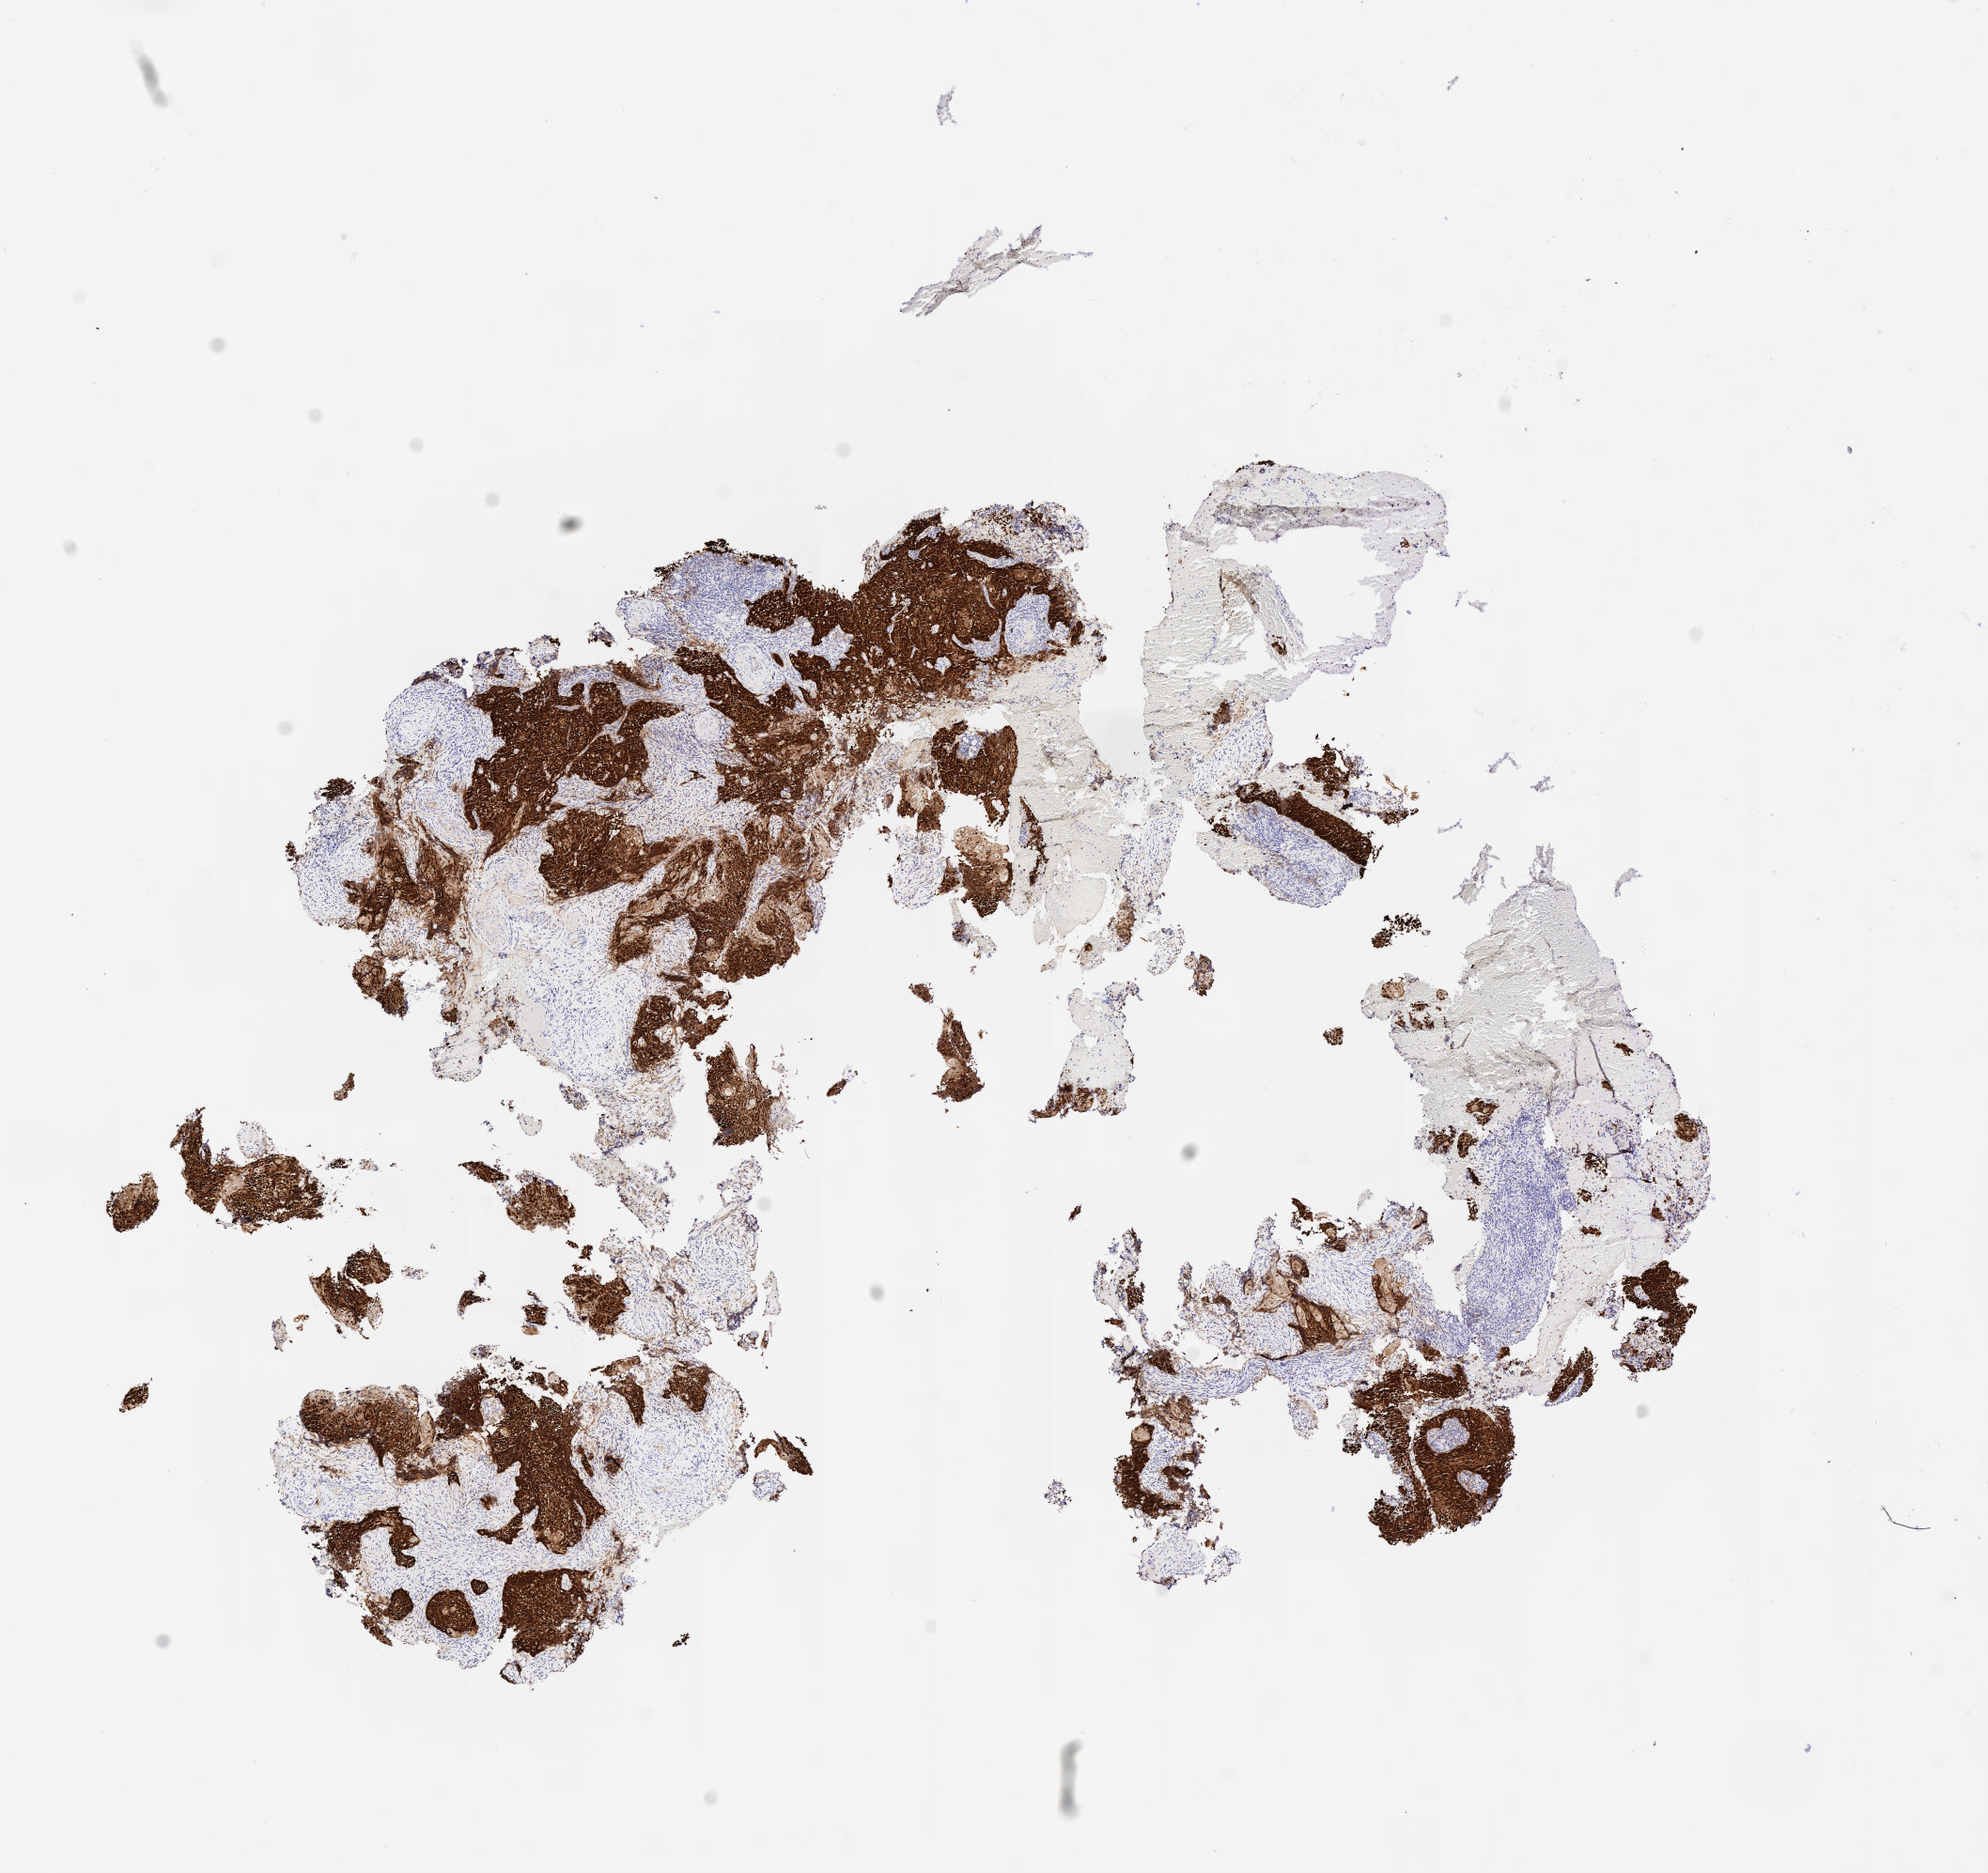
Immunohistochemistry (IHC) whole-slide image stained for p16 (p16INK4a) — shown as a low-resolution overview of the whole scanned area (about 8.6 x 8.1 mm), specimen: tumor tissue, site: cervix. Patient female; age 58 years.
• diagnosis: Squamous cell carcinoma, large cell, nonkeratinizing, NOS